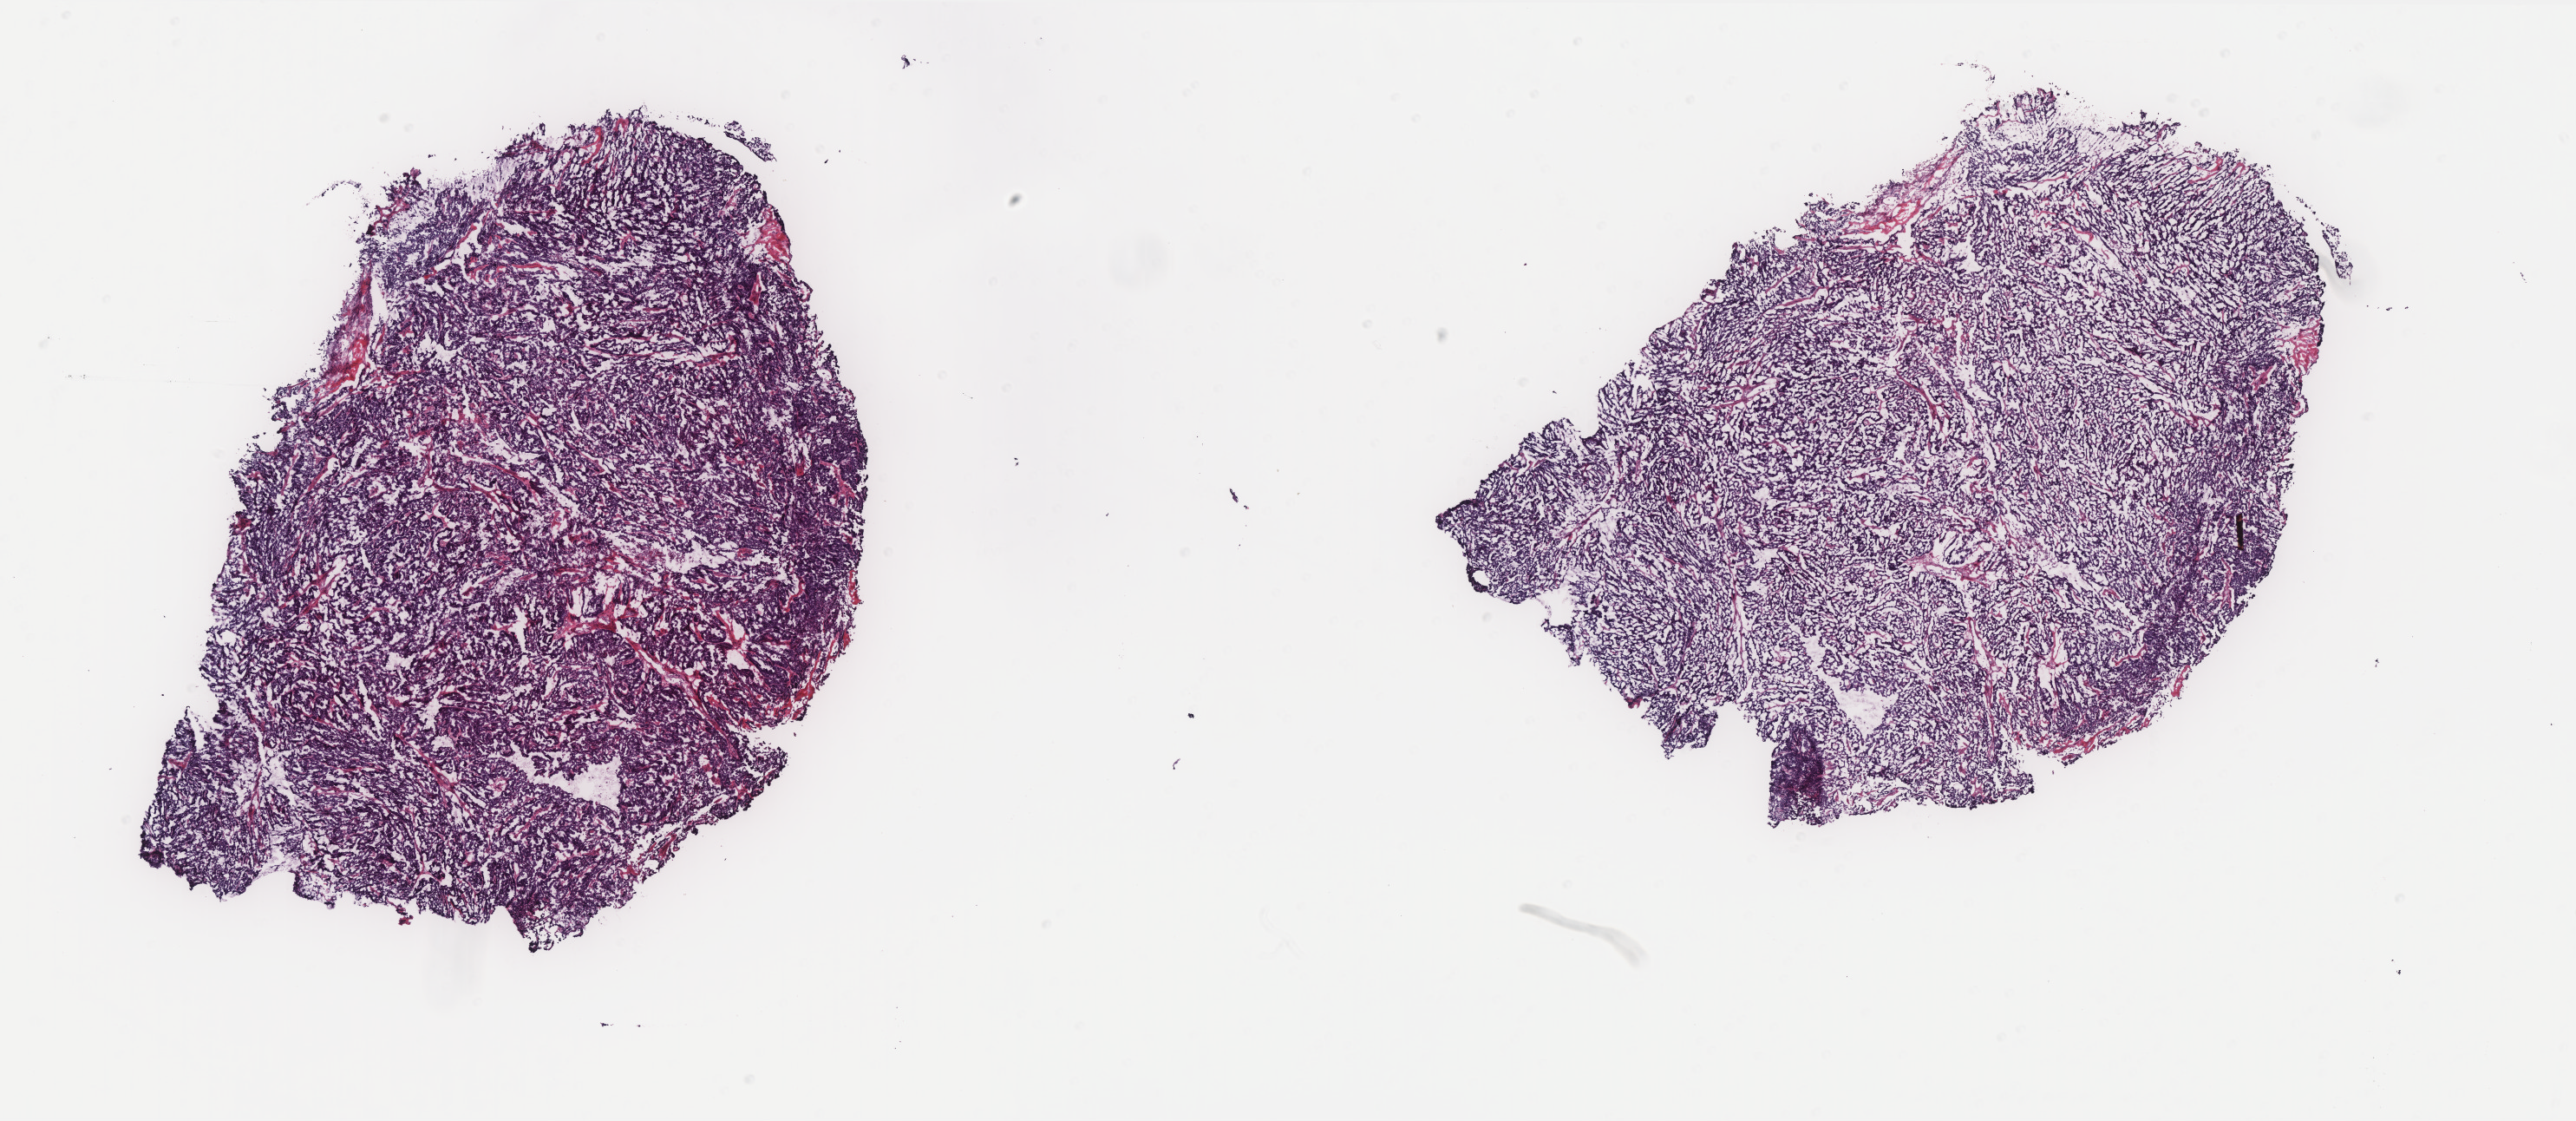
Whole-slide histology image, H&E — whole scanned area (about 23.8 x 10.4 mm) shown as a low-resolution overview. Frozen section from the top of the tissue portion. Primary tumour sample from the uterus. Female, age 77 years at initial diagnosis. Histologic grade: G3 (poorly differentiated). Pathologist review of this section (percent, as recorded): tumour cells 93%, tumour nuclei 94%, normal cells 0%, stromal cells 5%, necrosis 2%. Inflammatory infiltration, as recorded: lymphocyte infiltration 1%, monocyte infiltration 1%, neutrophil infiltration 1%.
FIGO stage: IB. Pathologic diagnosis: Serous cystadenocarcinoma, NOS (endometrium). Lymph nodes positive (case pathology): 0 of 24 examined.